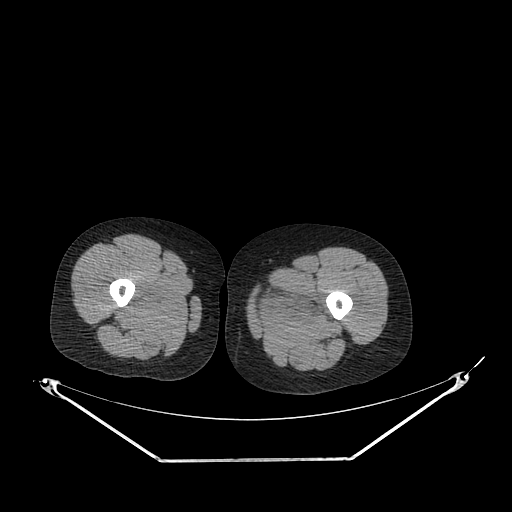
CT of an extremity soft-tissue mass (from a PET/CT study), one axial slice. Slice 225 of 267 in the series (ordered by position). Reconstruction kernel SOFT. Soft-tissue window (W 400 / L 40 HU). 3.75 mm slice thickness. 512 × 512 image matrix, field of view 500 × 500 mm. Female patient. From the clinical record (not read from this slice): histological type: pleiomorphic leiomyosarcoma; grade: intermediate; site of the primary tumour: left thigh.
Outlined on this slice (expert contour drawn on MRI and transferred to this co-registered scan by the dataset authors):
- gross tumour volume including surrounding oedema: bounding box (x1, y1, x2, y2) in pixels: (258, 281, 323, 320)